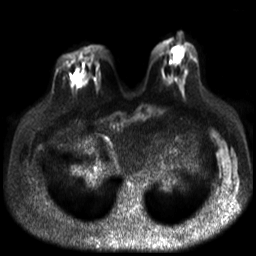
Breast MRI, one axial slice; position 12 of 30 along the scan axis; diffusion-weighted series; image 2 of 4 stored at this slice position (different b-values; order by instance number); 3 T; 4 mm slice thickness; 256 × 256 image matrix. Female patient.
Annotated regions visible in this slice (expert manual segmentation):
- tumour on diffusion-weighted imaging: bounding box [x1, y1, x2, y2] px = [71, 74, 83, 88]